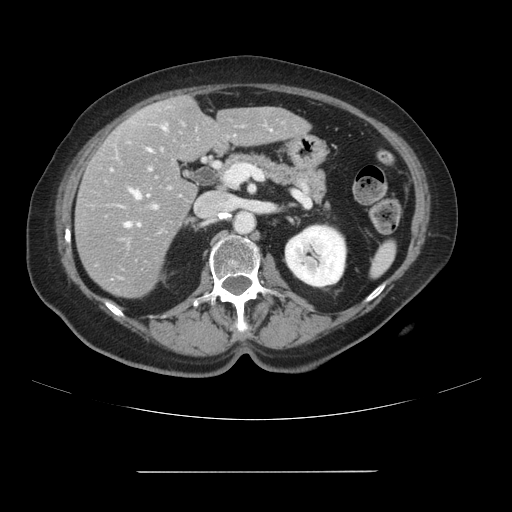
Contrast-enhanced abdominal CT, one axial slice; position 45 of 111 along the scan axis; 120 kVp; intravenous contrast given; soft-tissue window (W 400 / L 40 HU); 512 × 512 image matrix, field of view 400 × 400 mm. Female patient, age 74 years. From the clinical record (not read from this slice): diagnosis: colorectal cancer liver metastases, imaged before liver resection; multiple liver metastases: yes; largest metastasis: 1.1 cm; disease in both lobes: yes.
Annotated regions visible in this slice (manually delineated by an expert):
- hepatic veins: bounding box <125,126,166,227> (left, top, right, bottom; pixels)
- liver: <75,97,309,298>
- planned liver remnant (the part of the liver to remain after resection): <141,97,309,162>
- portal vein (with intrahepatic branches): <153,206,157,208>